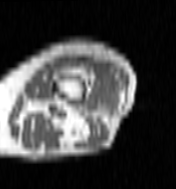
MRI of an extremity soft-tissue mass, one axial slice. Slice 23 of 100 in the series (ordered by position). MR volume resampled by the dataset authors to the PET/CT grid (not the native acquisition matrix). 176 × 189 image matrix, field of view 172 × 185 mm. Female patient. From the clinical record (not read from this slice): histological type: undifferentiated – high grade; grade: high; site of the primary tumour: left thigh.
Outlined on this slice (expert contour drawn on MRI and transferred to this co-registered scan by the dataset authors):
- gross tumour volume including surrounding oedema: box from (x=96, y=86) to (x=113, y=99) px